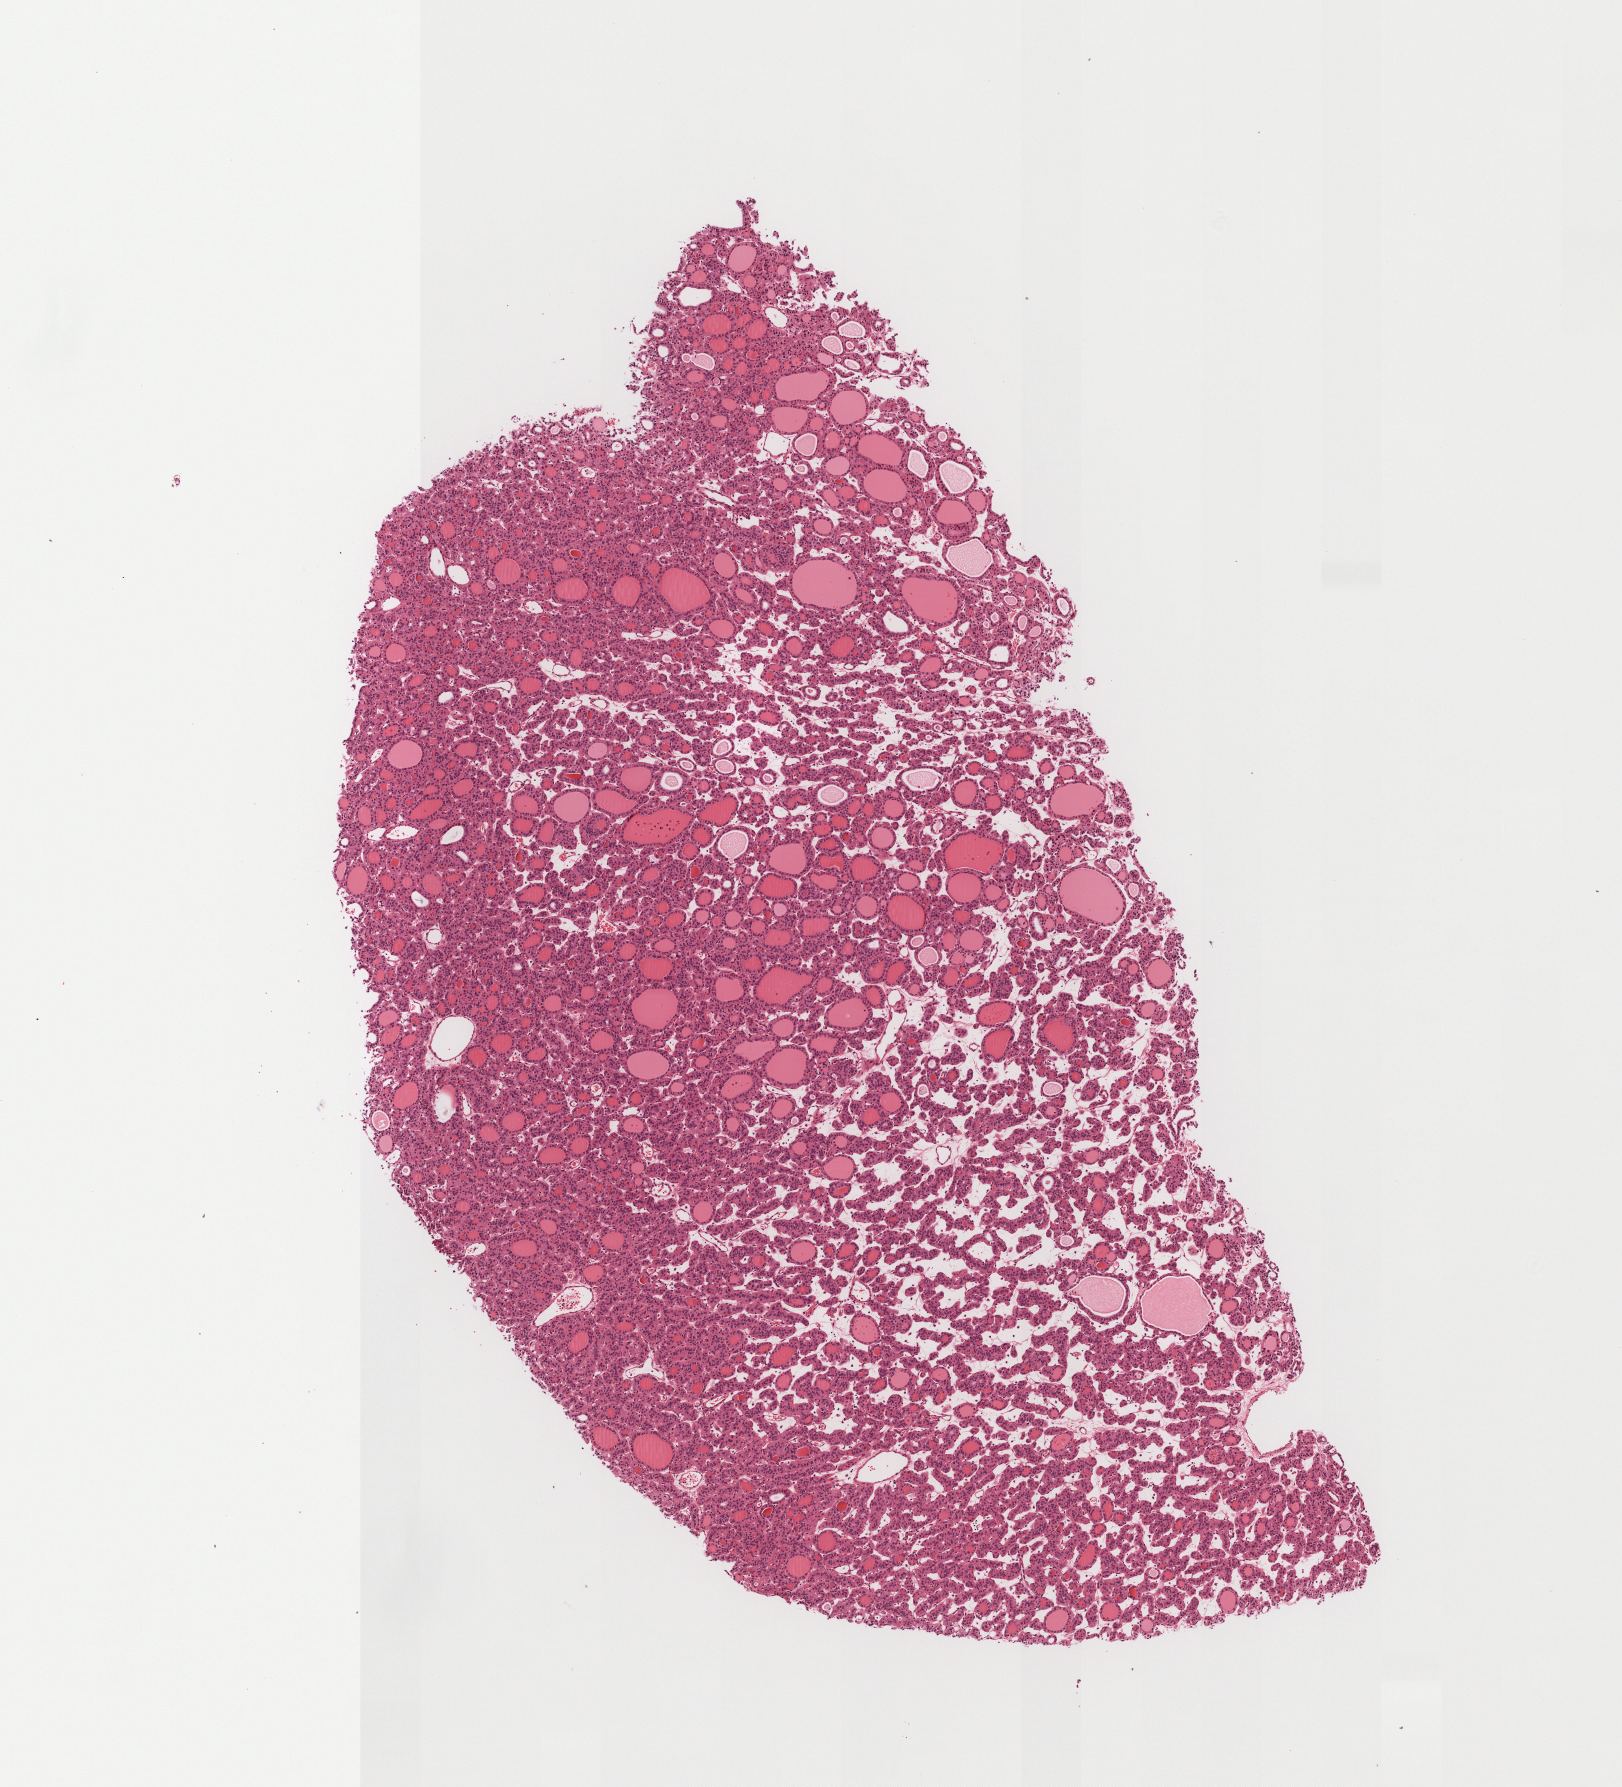
H&E-stained whole-slide image — whole scanned area (about 6.5 x 7.2 mm, acquisition: 40x scan) shown as a low-resolution overview; formalin-fixed paraffin-embedded (FFPE) diagnostic section; thyroid, primary tumour sample. Female, age 20 years at initial diagnosis.
Laterality: right. AJCC pathologic stage: I (7th edition). TNM: T1b N0 MX. Lymph nodes positive (case pathology): 0 of 5 examined. Diagnosis: Papillary carcinoma, follicular variant (thyroid gland).